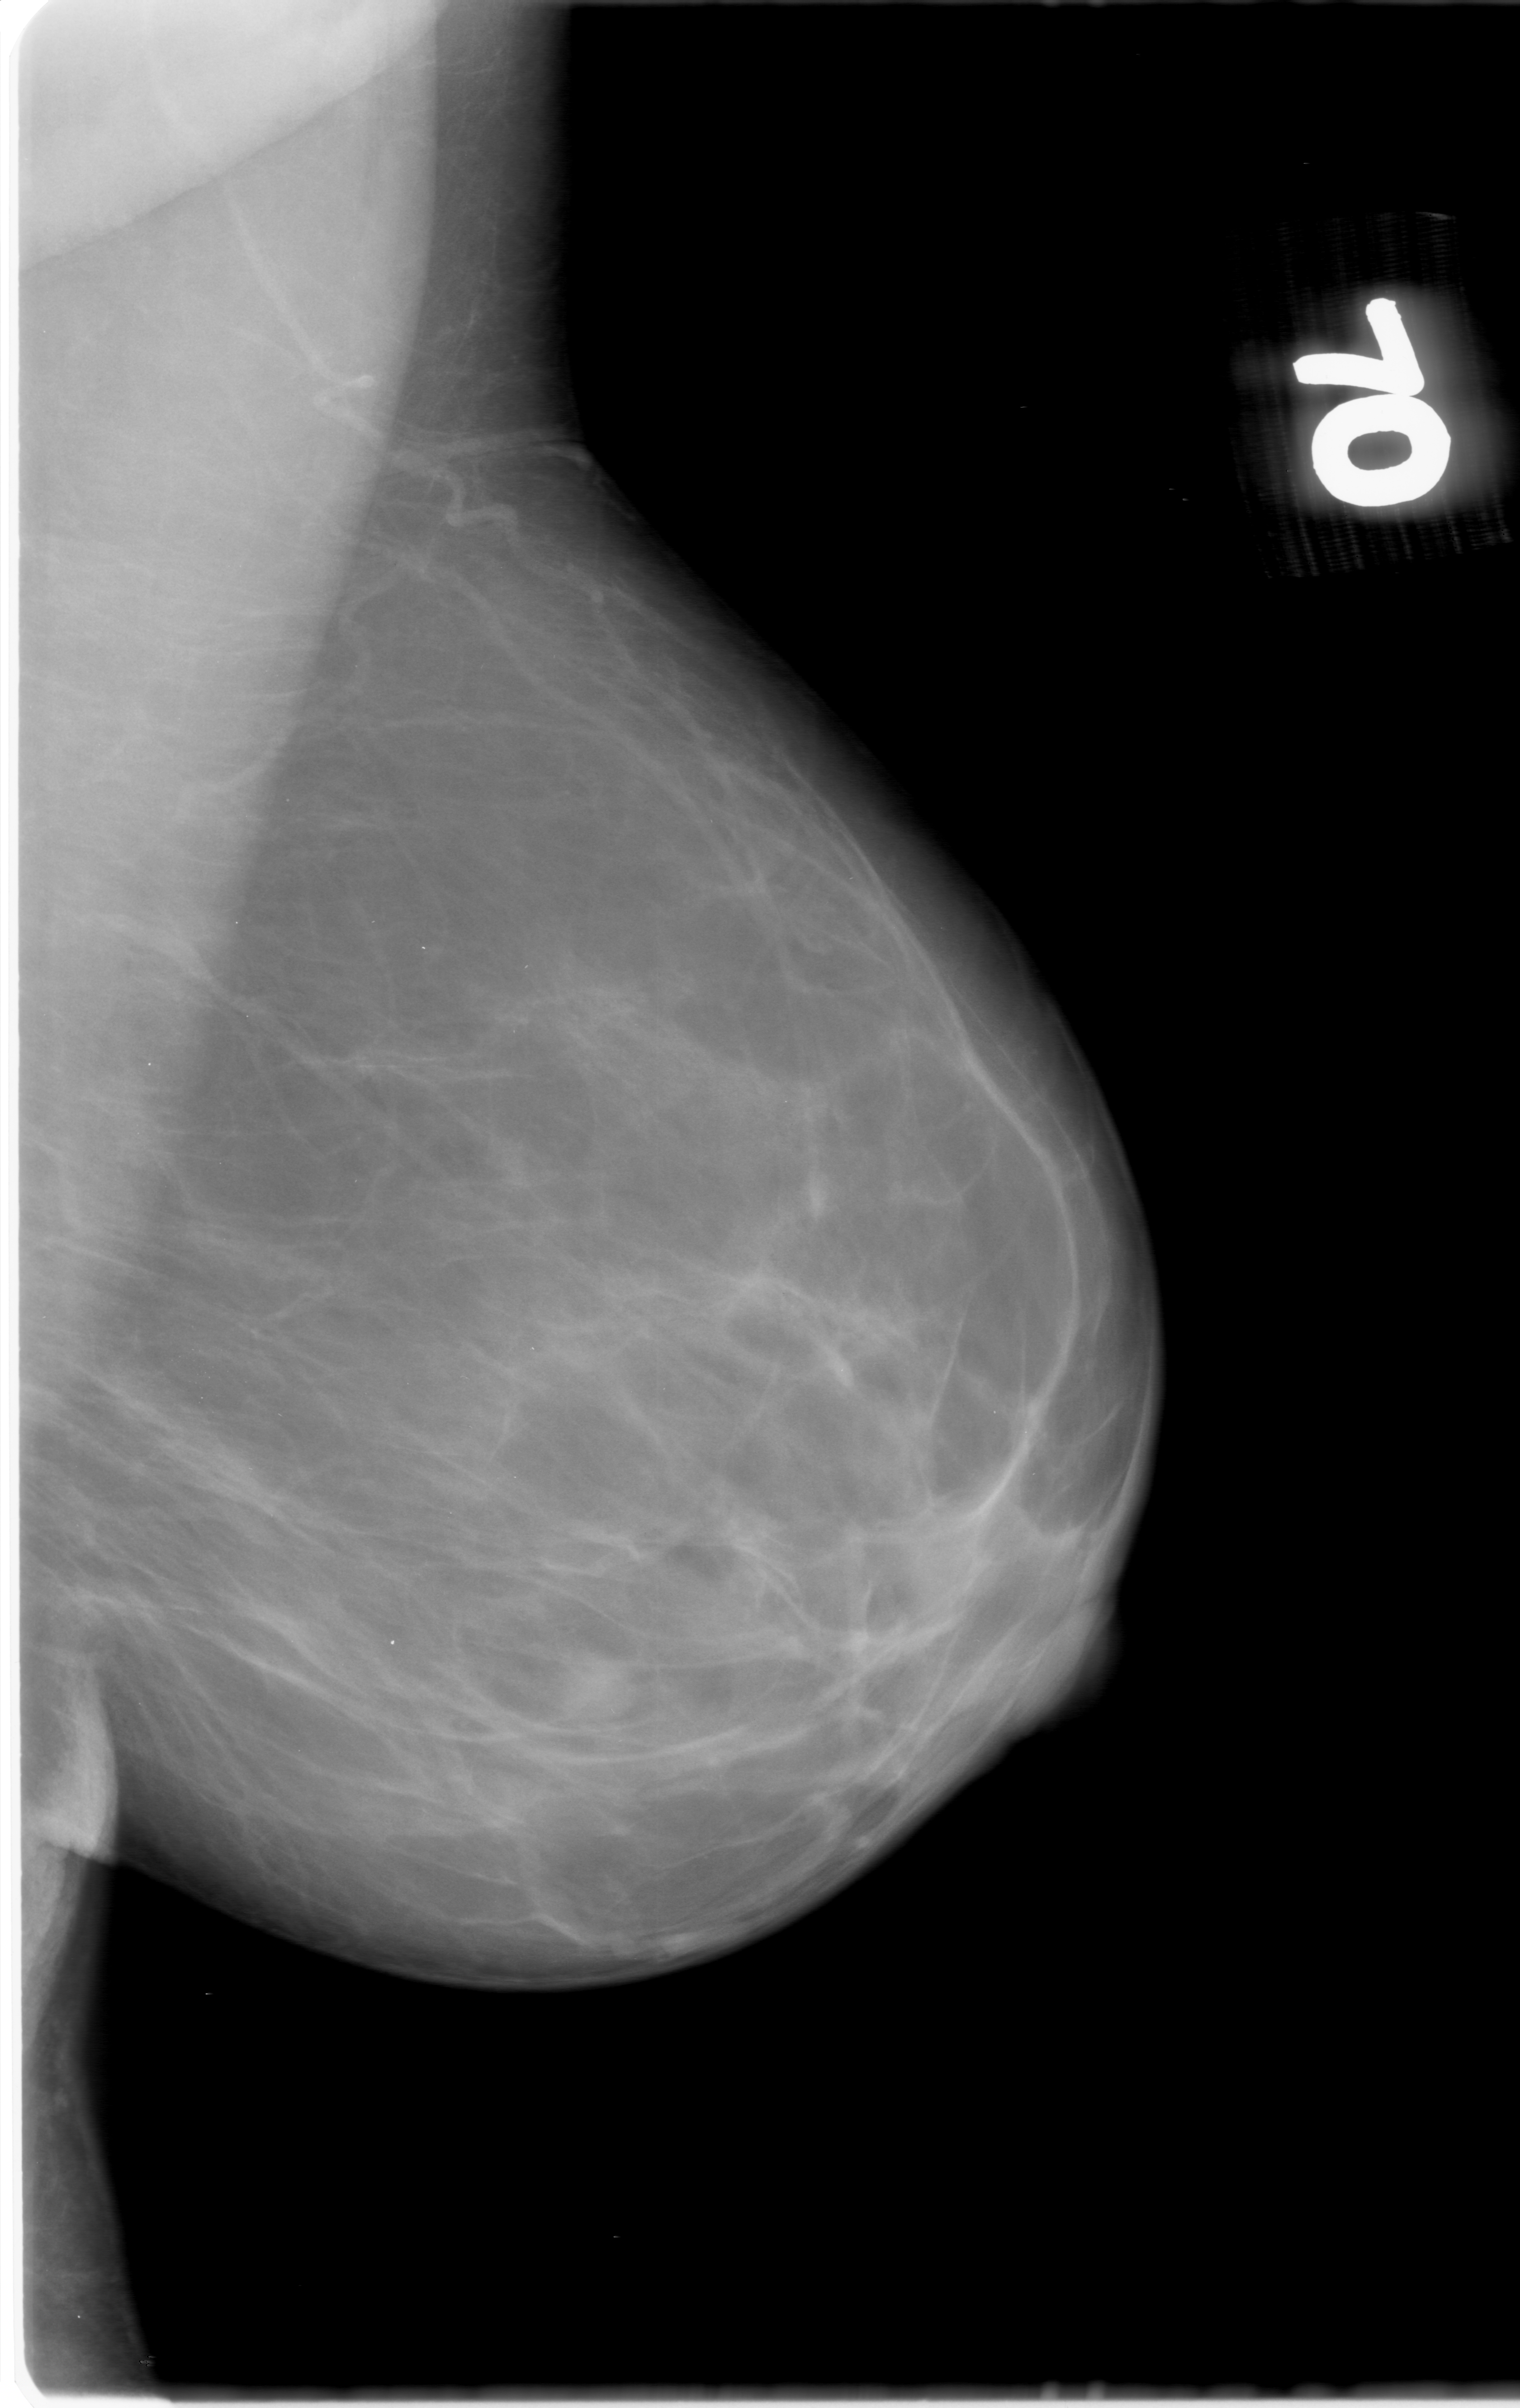
Scanned film-screen mammogram; left breast; mediolateral oblique (MLO) view; BI-RADS breast density category 1 (scale 1–4); 1520 × 2408 image matrix.
Marked abnormalities (boxes around the expert regions of interest):
- mass, shape round, margins obscured; BI-RADS assessment category 0 (incomplete: needs additional imaging); subtlety rating 4 on a 1 (subtle) to 5 (obvious) scale; pathology result (as recorded, not read from the image): benign: bounding box (x1, y1, x2, y2) in pixels: (512, 1633, 647, 1728)